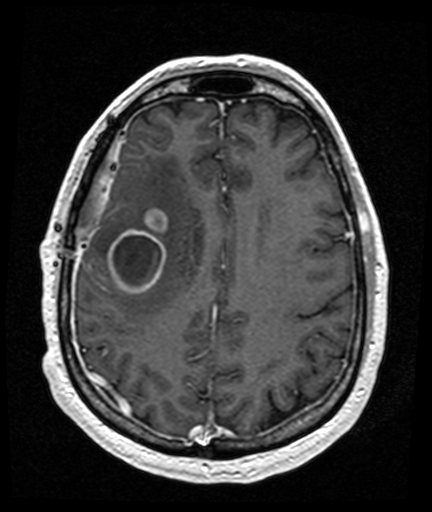
Brain MRI from a brain-tumour surgery series, one axial slice. Slice 55 of 176 in the series (ordered by position). T1-weighted post-contrast. 1 mm slice thickness. 432 × 512 image matrix. From the clinical record (not read from this slice): histopathology: Glioblastoma; WHO grade: 4; IDH mutation: no; tumour location: Right Frontal Temporal, Posterior Sylvian Fissure.
Outlined on this slice (manually delineated by an expert):
- tumour: bounding box [x1, y1, x2, y2] px = [109, 210, 168, 294]